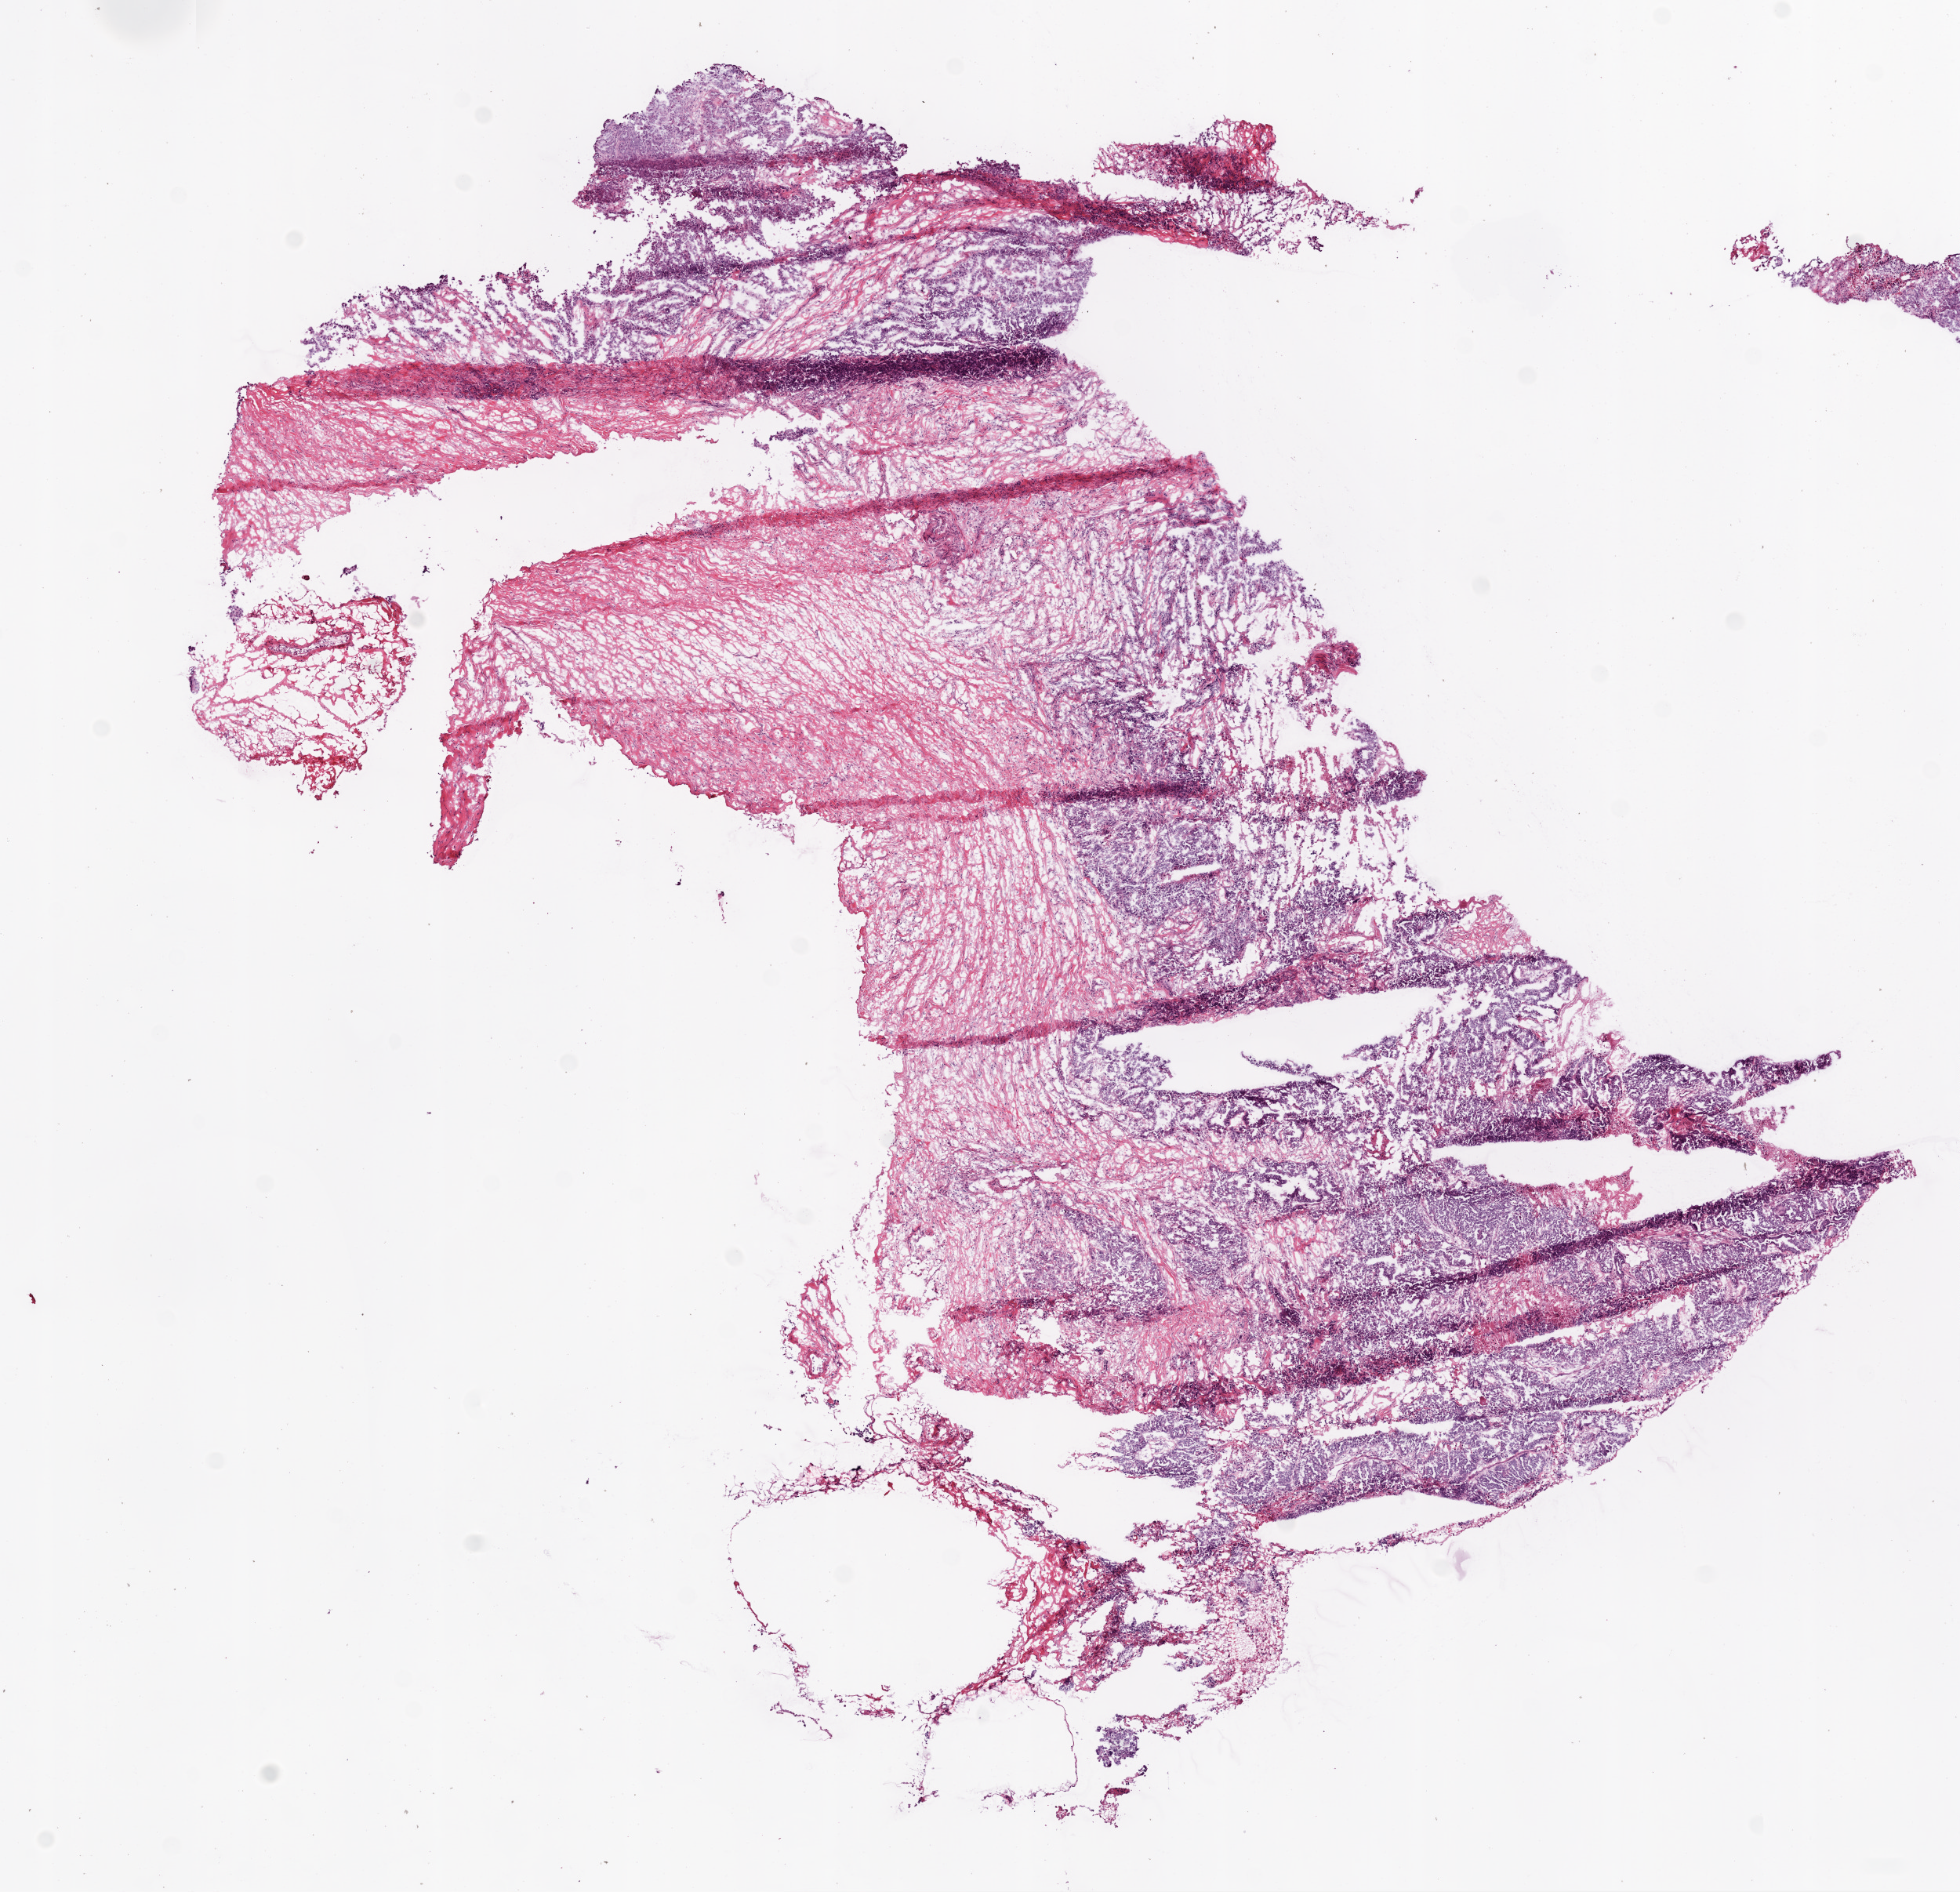
H&E-stained whole-slide image, shown as a low-resolution overview of the whole scanned area (about 10.0 x 9.7 mm, slide scanned at 20x), frozen section from the bottom of the tissue portion, sample: recurrent tumour, ovary. Female, age 54 years at initial diagnosis. Slide review estimates, as recorded: tumour cells 50%, tumour nuclei 90%, normal cells 0%, stromal cells 30%, necrosis 20%.
* this section: recurrent tumour
* patient diagnosis: Serous cystadenocarcinoma, NOS